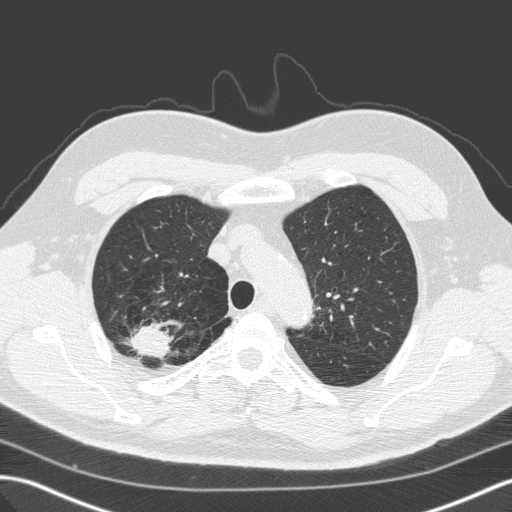
Axial slice from a low-dose chest CT screening exam; baseline screening round; lung window (W 1500 / L -600 HU); 2 mm slice thickness; slice 29 of 149 in the series; 512 × 512 image matrix, field of view 357 × 357 mm. Male participant, aged 59 years at enrolment. Former smoker at enrolment.
- Lesion marked by an expert reader, box from (x=118, y=312) to (x=180, y=369) px.
- The exam's reader record, not a measurement of the box and not confirmed to be the same lesion: non-calcified nodule or mass ≥4 mm, right upper lobe, 28 × 25 mm, spiculated (stellate) margins, soft tissue attenuation.
- Official screen result: positive, change unspecified: nodule(s) >= 4 mm or enlarging nodule(s), mass(es), or other non-specific abnormalities suspicious for lung cancer.
- Participant outcome: lung cancer diagnosed 64 days after this screen — large cell carcinoma, NOS, right upper lobe, undifferentiated (G4), stage IA (AJCC 6th edition), 25 mm at pathology.